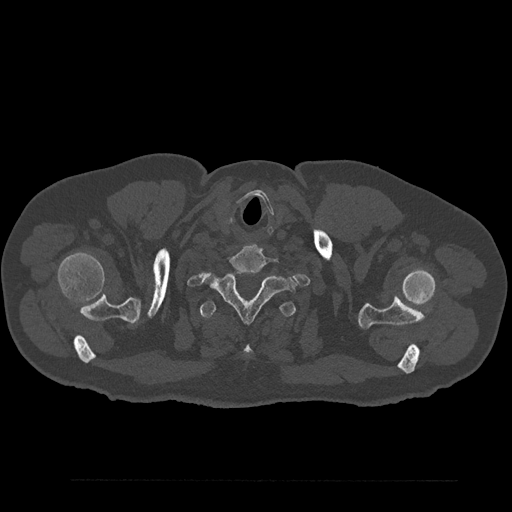
CT including the spine, one axial slice. Position 751 of 797 along the scan axis. Bone window (W 1800 / L 400 HU). 0.5 mm slice thickness. 512 × 512 image matrix. Patient: male, 61 years. Case-level facts recorded for this patient, not image findings: primary cancer: prostate.
Annotated regions visible in this slice (semi-automatically segmented with operator editing):
- T1 vertebra: bounding box [x1, y1, x2, y2] px = [206, 269, 296, 323]
- T2 vertebra: [200, 300, 296, 356]